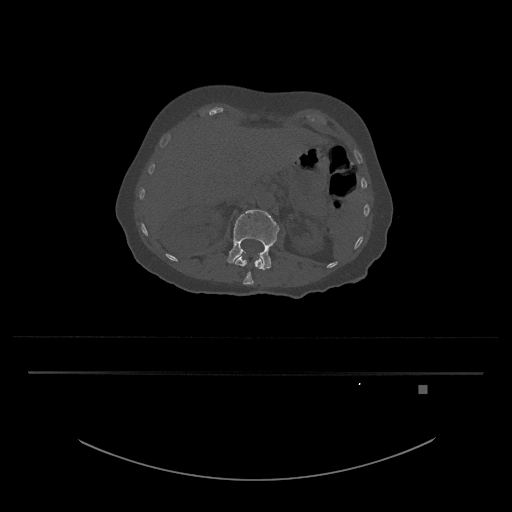
CT including the spine, one axial slice. Position 516 of 797 along the scan axis. Bone window (W 1800 / L 400 HU). 0.5 mm slice thickness. 512 × 512 image matrix, field of view 500 × 500 mm. Patient: female, 57 years. From the clinical record (not read from this slice): primary cancer: cervical.
Annotated regions visible in this slice (semi-automatic segmentation, software-assisted and operator-edited):
- L1 vertebra: box from (x=235, y=252) to (x=263, y=285) px